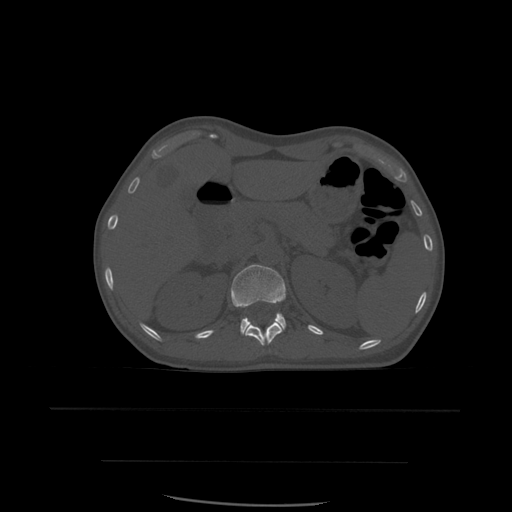
CT including the spine, one axial slice; slice 262 of 574 in the series (ordered by position); bone window (W 1800 / L 400 HU); 1.25 mm slice thickness; 512 × 512 image matrix. Patient age 48 years. From the clinical record (not read from this slice): primary cancer: lung.
Structures marked on this image (semi-automatic segmentation, software-assisted and operator-edited):
- L1 vertebra: bounding box (x1, y1, x2, y2) in pixels: (231, 265, 287, 335)
- T12 vertebra: (245, 322, 283, 346)